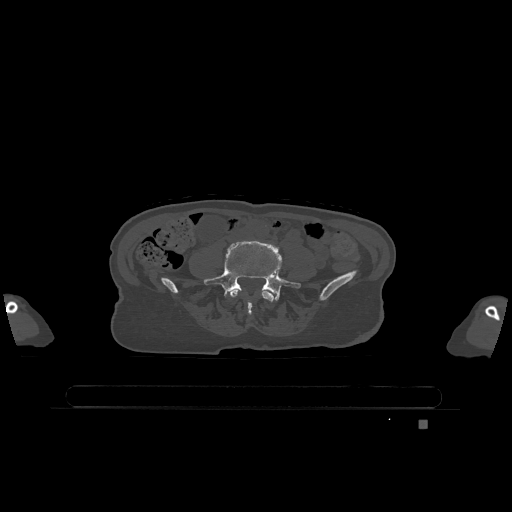
CT including the spine, one axial slice. Position 257 of 1317 along the scan axis. Bone window (W 1800 / L 400 HU). 0.5 mm slice thickness. 512 × 512 image matrix. Patient: female, 74 years. From the clinical record (not read from this slice): primary cancer: lung.
Structures marked on this image (semi-automatically segmented with operator editing):
- L4 vertebra: bounding box [x1, y1, x2, y2] px = [230, 289, 274, 315]
- L5 vertebra: [204, 241, 301, 302]